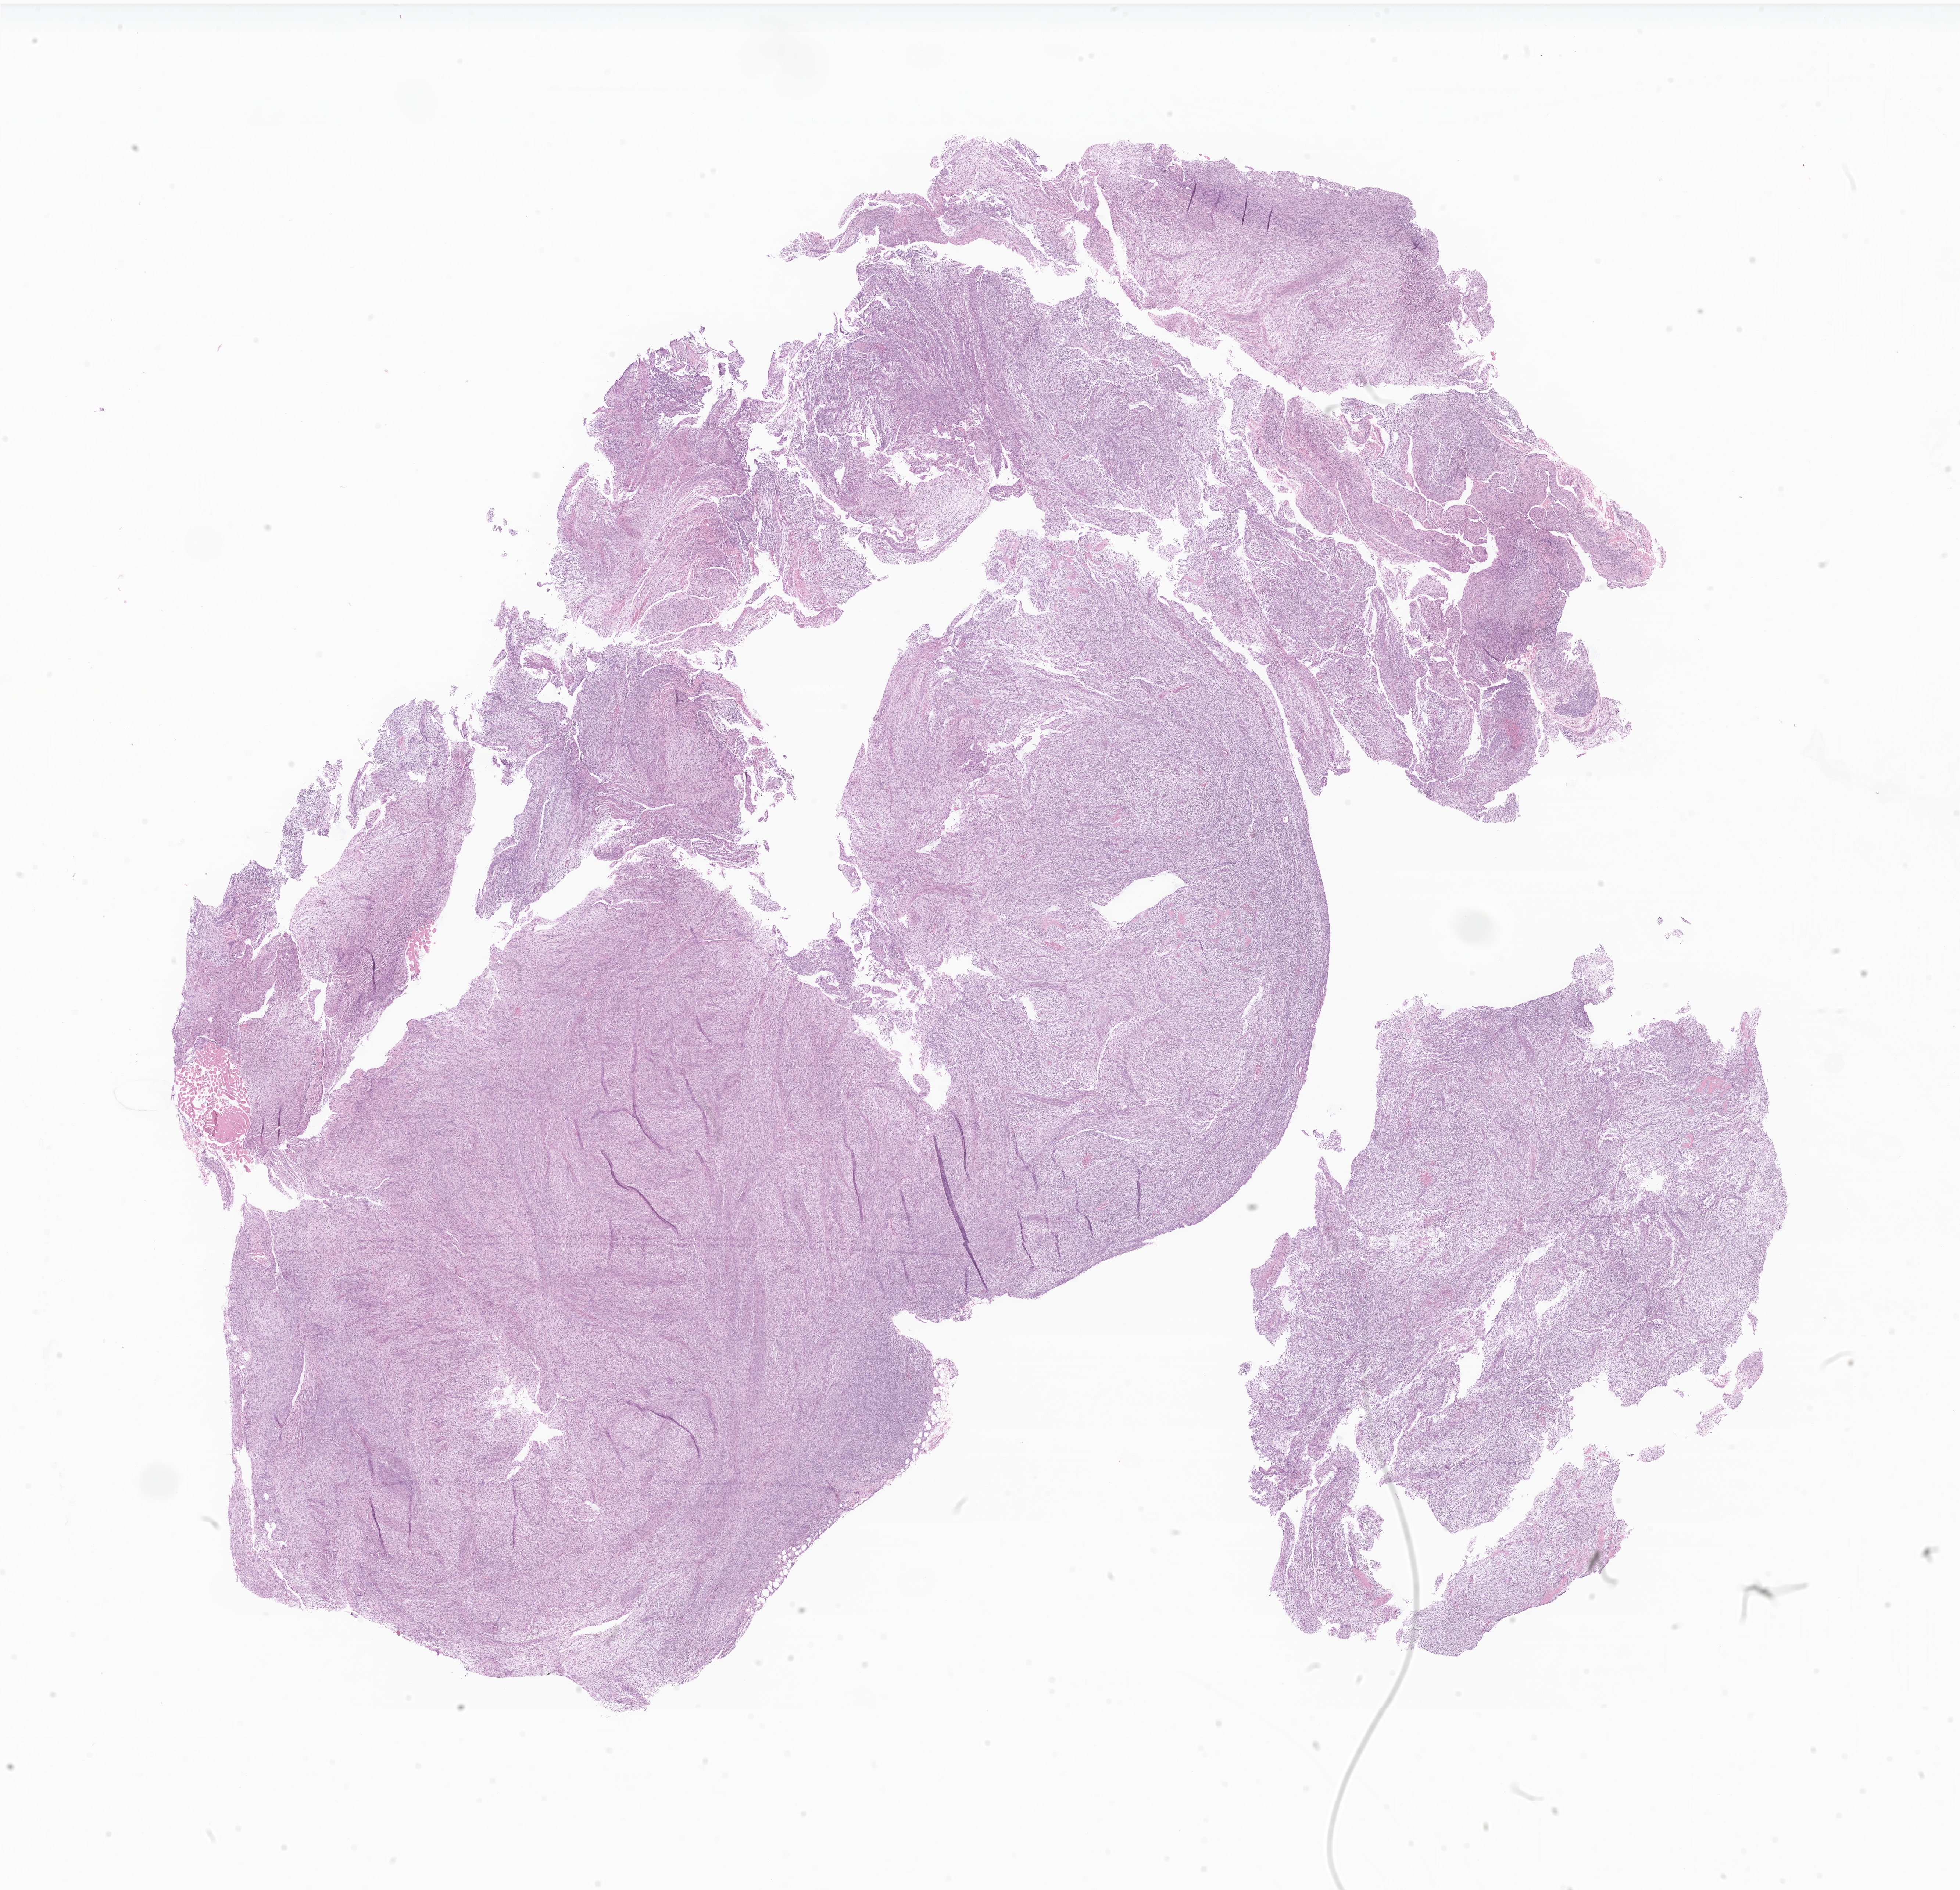
Hematoxylin and eosin (H&E) whole-slide image of tumor tissue from the soft tissue of lower extremity — whole scanned area (about 22.5 x 21.7 mm) shown as a low-resolution overview, formalin-fixed paraffin-embedded section. Patient: male, age 86 months (7 years 2 months).
• diagnosis: Synovial sarcoma, NOS